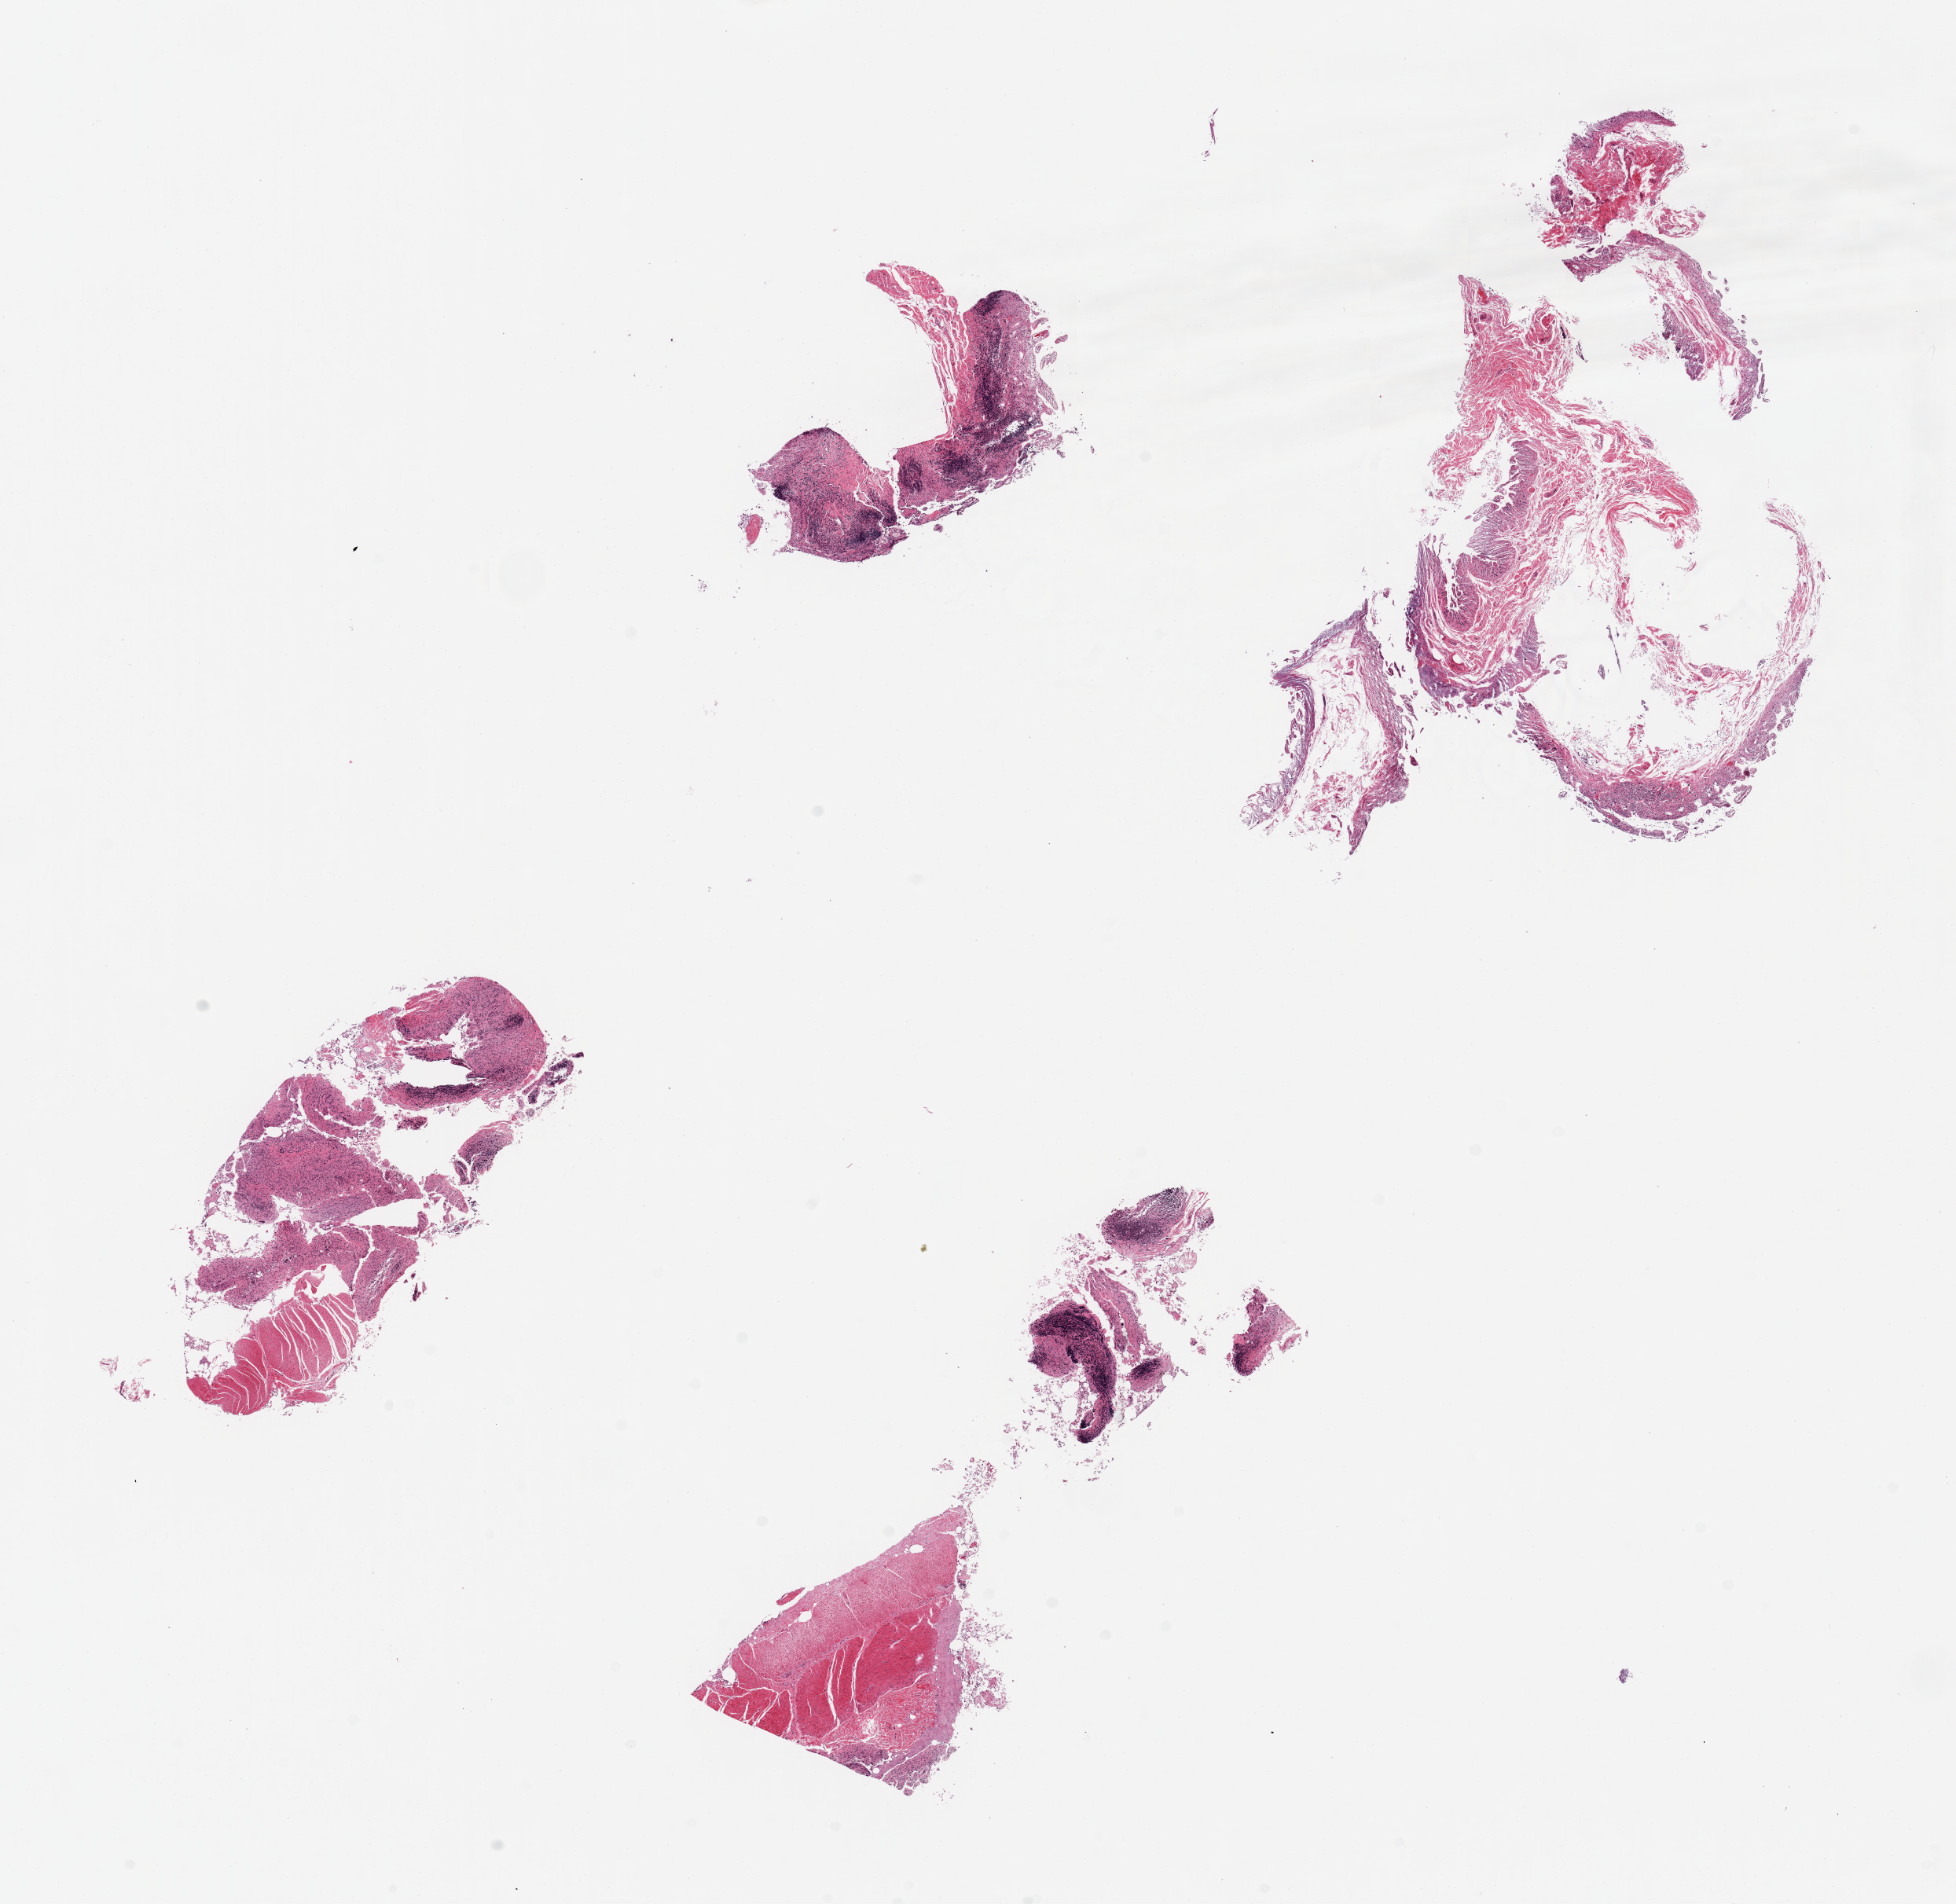
H&E whole-slide image, brightfield, a low-resolution overview of the entire scanned area, about 19.7 x 19.2 mm. PAXgene-fixed, paraffin-embedded tissue. Section of ileum (target tissue). Donor tissue sample. Donor sex: female.
• review note (as recorded): 4 pieces; up to 8x5mm; small amount of lymphoid tissue collected; extraneous muscle also collected